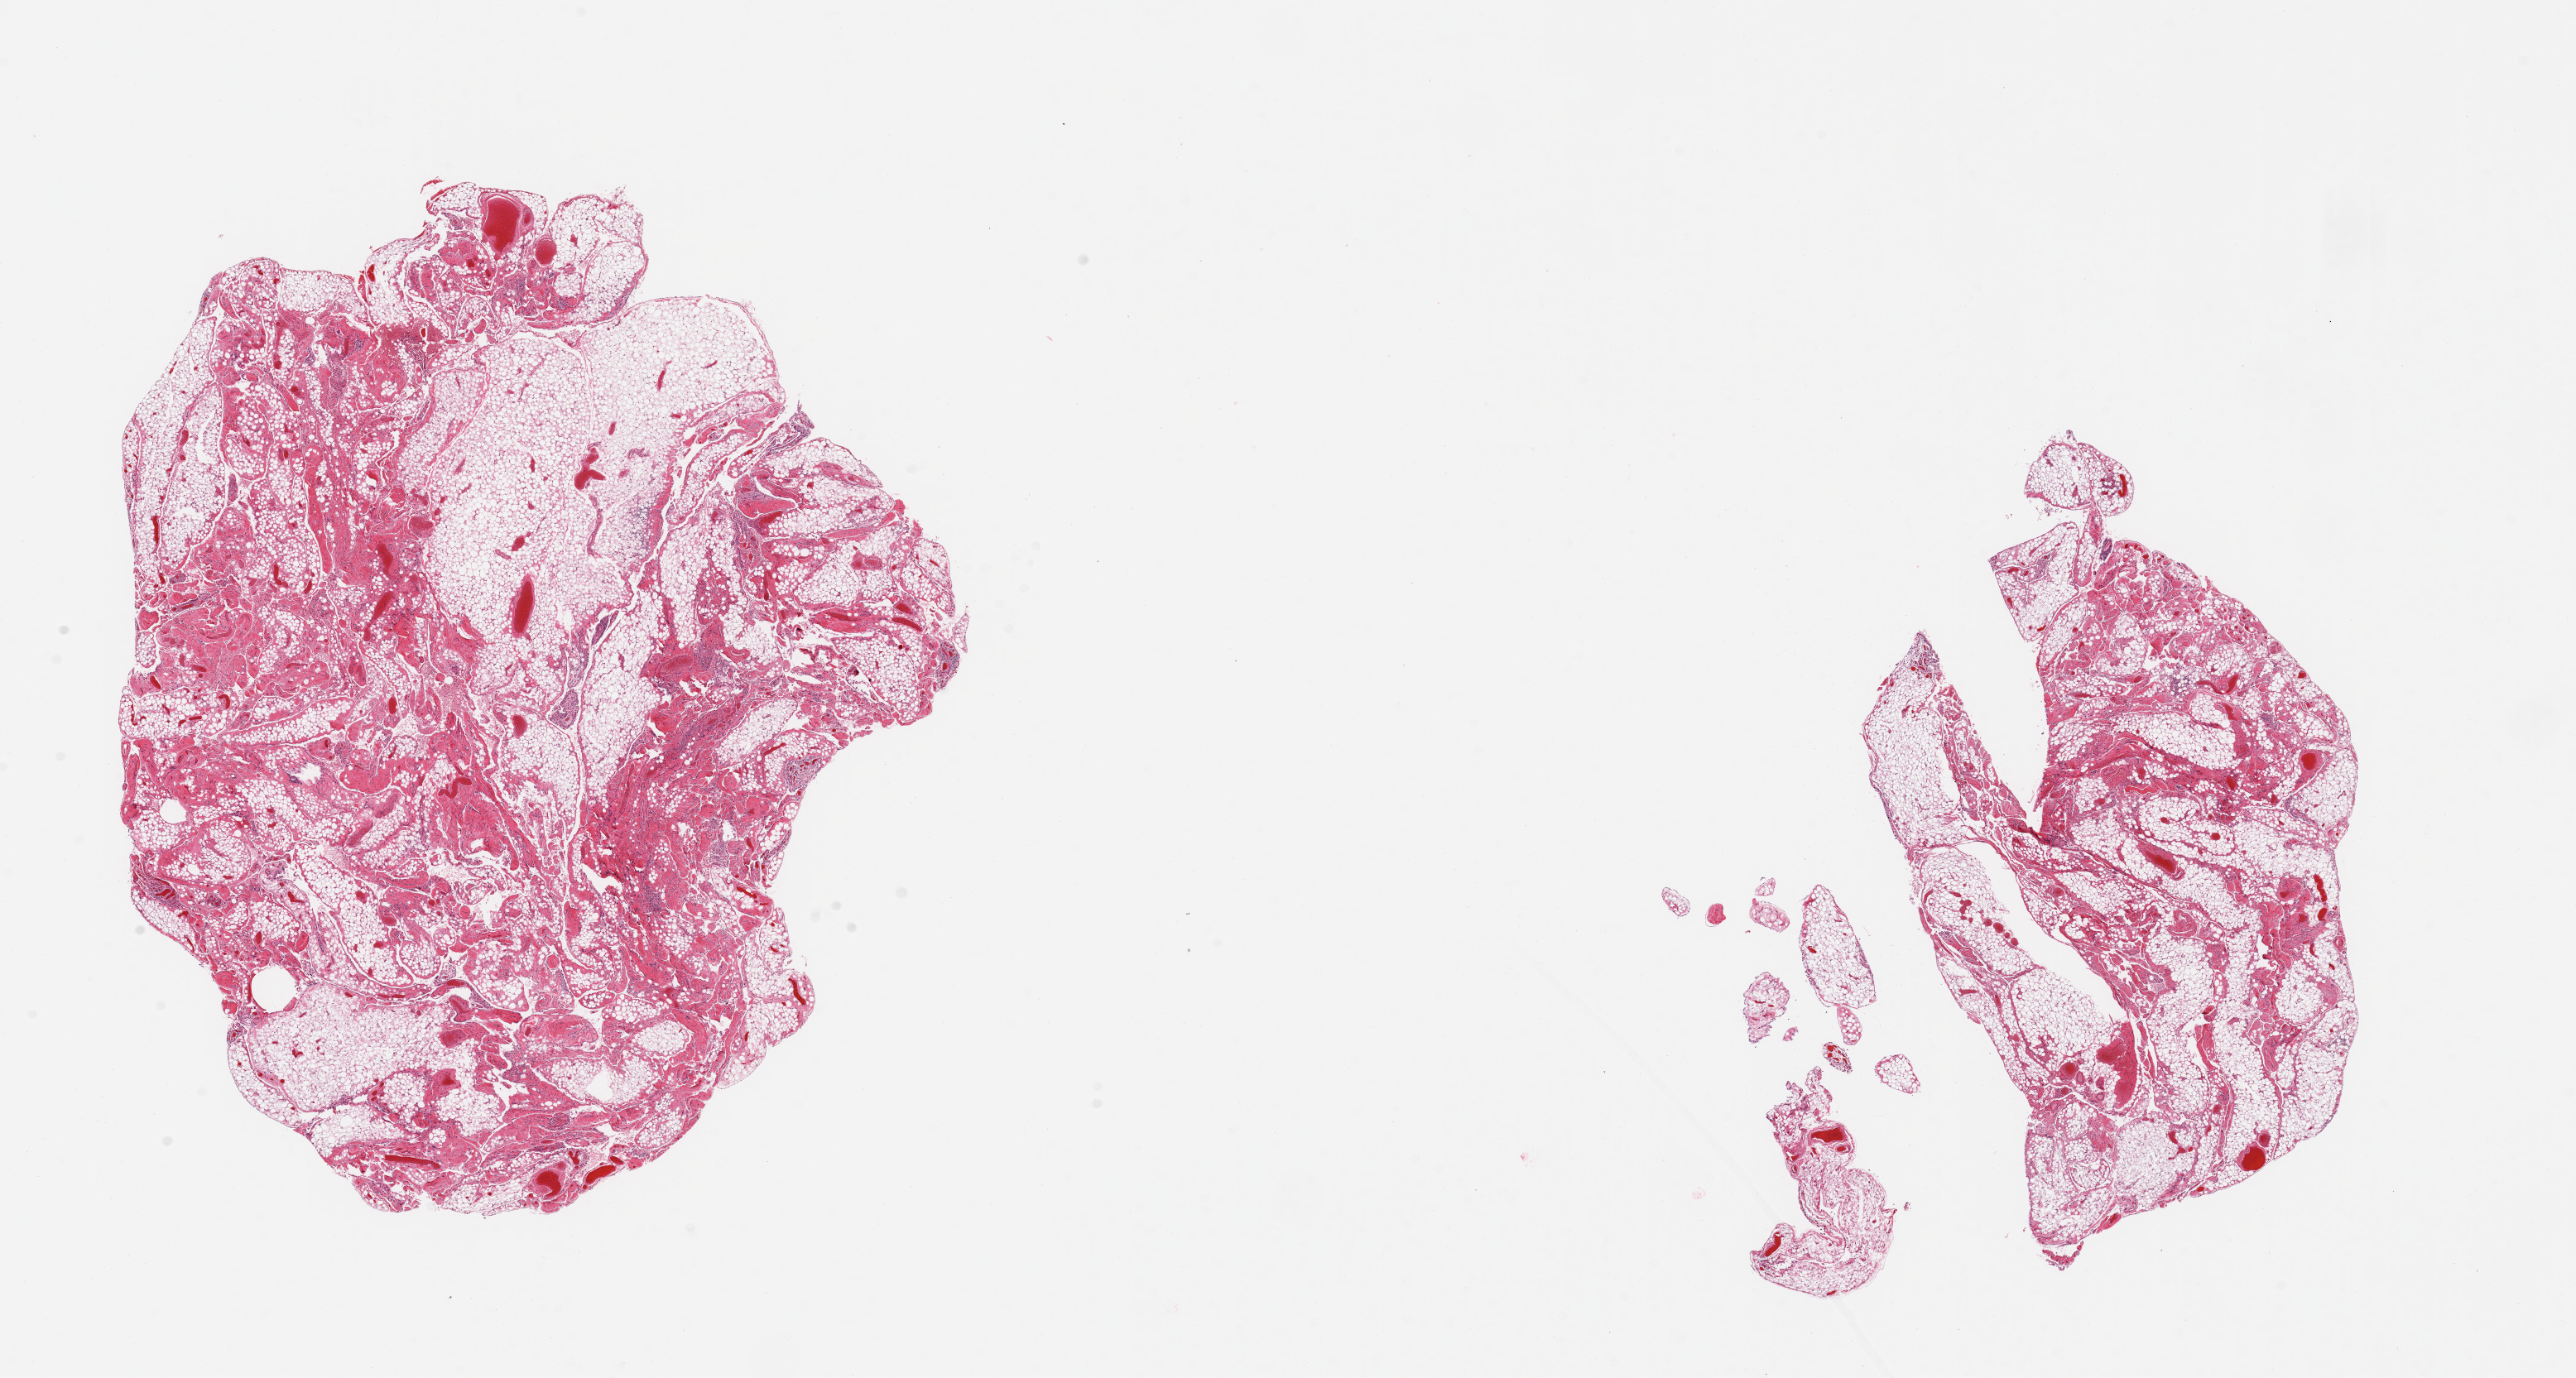
Hematoxylin and eosin (H&E) whole-slide image, low-resolution overview of the scanned area, about 24.6 x 13.2 mm. PAXgene-fixed, paraffin-embedded tissue. Sampled site (target tissue): omentum. Tissue donor sample. Male donor.
* pathologist's review note for this sample: 2 pieces; one piece fragmented; mature adipose tissue with ~50% fibrous content